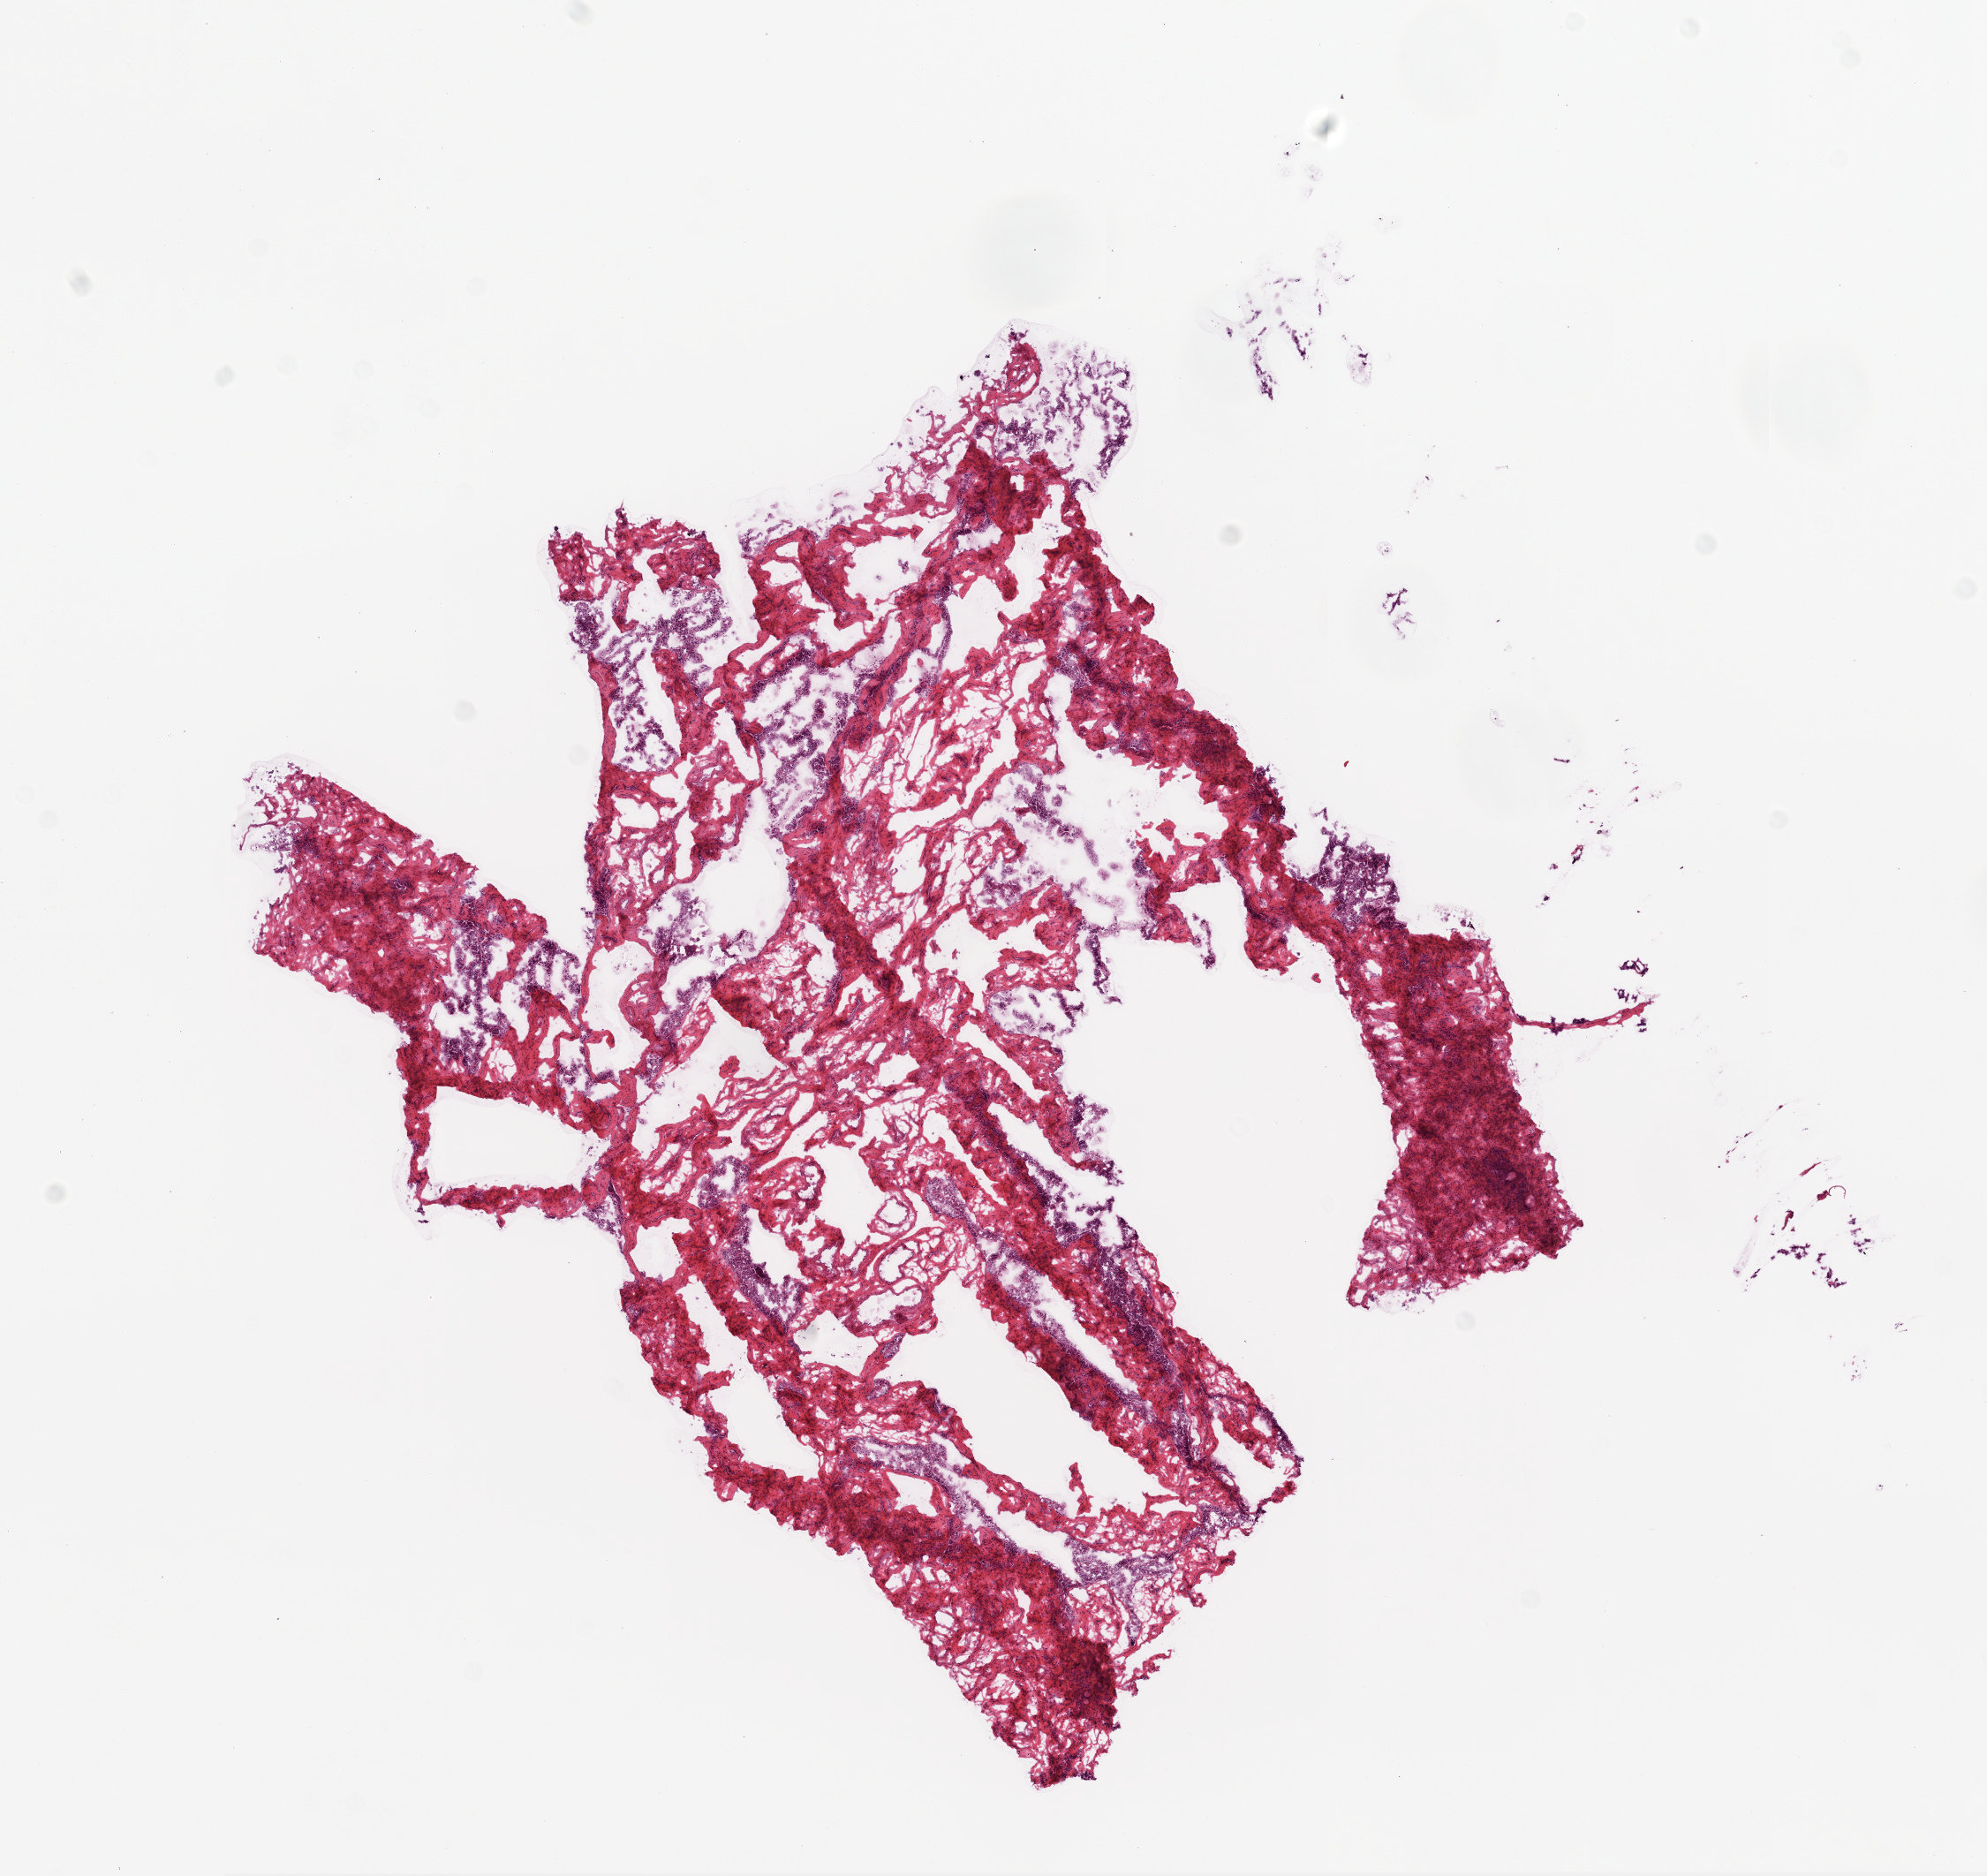
Digitized Hematoxylin and eosin (H&E) stained tissue section (whole slide) — whole scanned area (about 9.0 x 8.5 mm) shown as a low-resolution overview; frozen section from the bottom of the tissue portion; ovary, solid tissue normal (non-tumour tissue) sample. Female patient; age at initial diagnosis 48 years.
This section: solid tissue normal sample (biorepository sample class). Patient diagnosis: Serous cystadenocarcinoma, NOS.